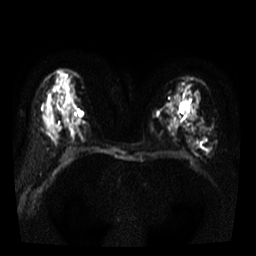
Breast MRI, one axial slice; position 21 of 38 along the scan axis; diffusion-weighted series; image 2 of 4 stored at this slice position (different b-values; order by instance number); 3 T; 5 mm slice thickness; 256 × 256 image matrix. Female patient.
Annotated regions visible in this slice (expert manual segmentation):
- tumour on diffusion-weighted imaging: bounding box (x1, y1, x2, y2) in pixels: (200, 139, 210, 151)